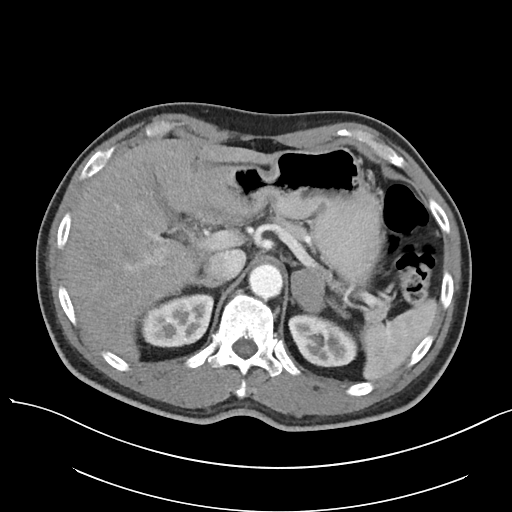
Contrast-enhanced abdominal CT, one axial slice; position 79 of 138 along the scan axis; reconstruction kernel I30f/3; intravenous contrast given; soft-tissue window (W 400 / L 40 HU); 5 mm slice thickness; 512 × 512 image matrix, field of view 400 × 400 mm. Male patient, age 63 years. Case-level facts recorded for this patient, not image findings: diagnosis: adrenocortical carcinoma; tumour side: left adrenal; tumour size at pathology: 4.5 cm; Ki-67 index: 12 %; stage (as recorded): 1.
Annotated regions visible in this slice (semi-automatic segmentation, software-assisted and operator-edited):
- mass: bounding box (x1, y1, x2, y2) in pixels: (291, 268, 325, 313)